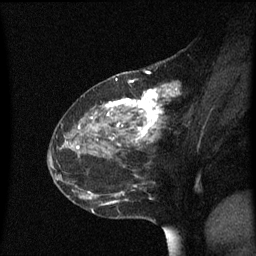
Breast MRI (dynamic contrast-enhanced), one sagittal slice; position 25 of 60 along the scan axis; dynamic contrast-enhanced series, image 2 of 3 at this slice position (ordered by acquisition); 1.5 T; TE 4.2 ms, TR 8.4 ms; 2 mm slice thickness; 256 × 256 image matrix, field of view 200 × 200 mm. Female patient, age 48 years. Case-level facts recorded for this patient, not image findings: setting: breast cancer imaged before/during neoadjuvant chemotherapy; receptor status: HR-positive, HER2-negative.
Structures marked on this image (semi-automatic segmentation, software-assisted and operator-edited):
- analysis volume of interest (the breast-tissue region the enhancement analysis was run in; not a lesion): bounding box (x1, y1, x2, y2) in pixels: (80, 78, 181, 221)
- tumour enhancement mask (voxels above the 70 % enhancement threshold inside the analysis volume of interest): (92, 85, 179, 196)